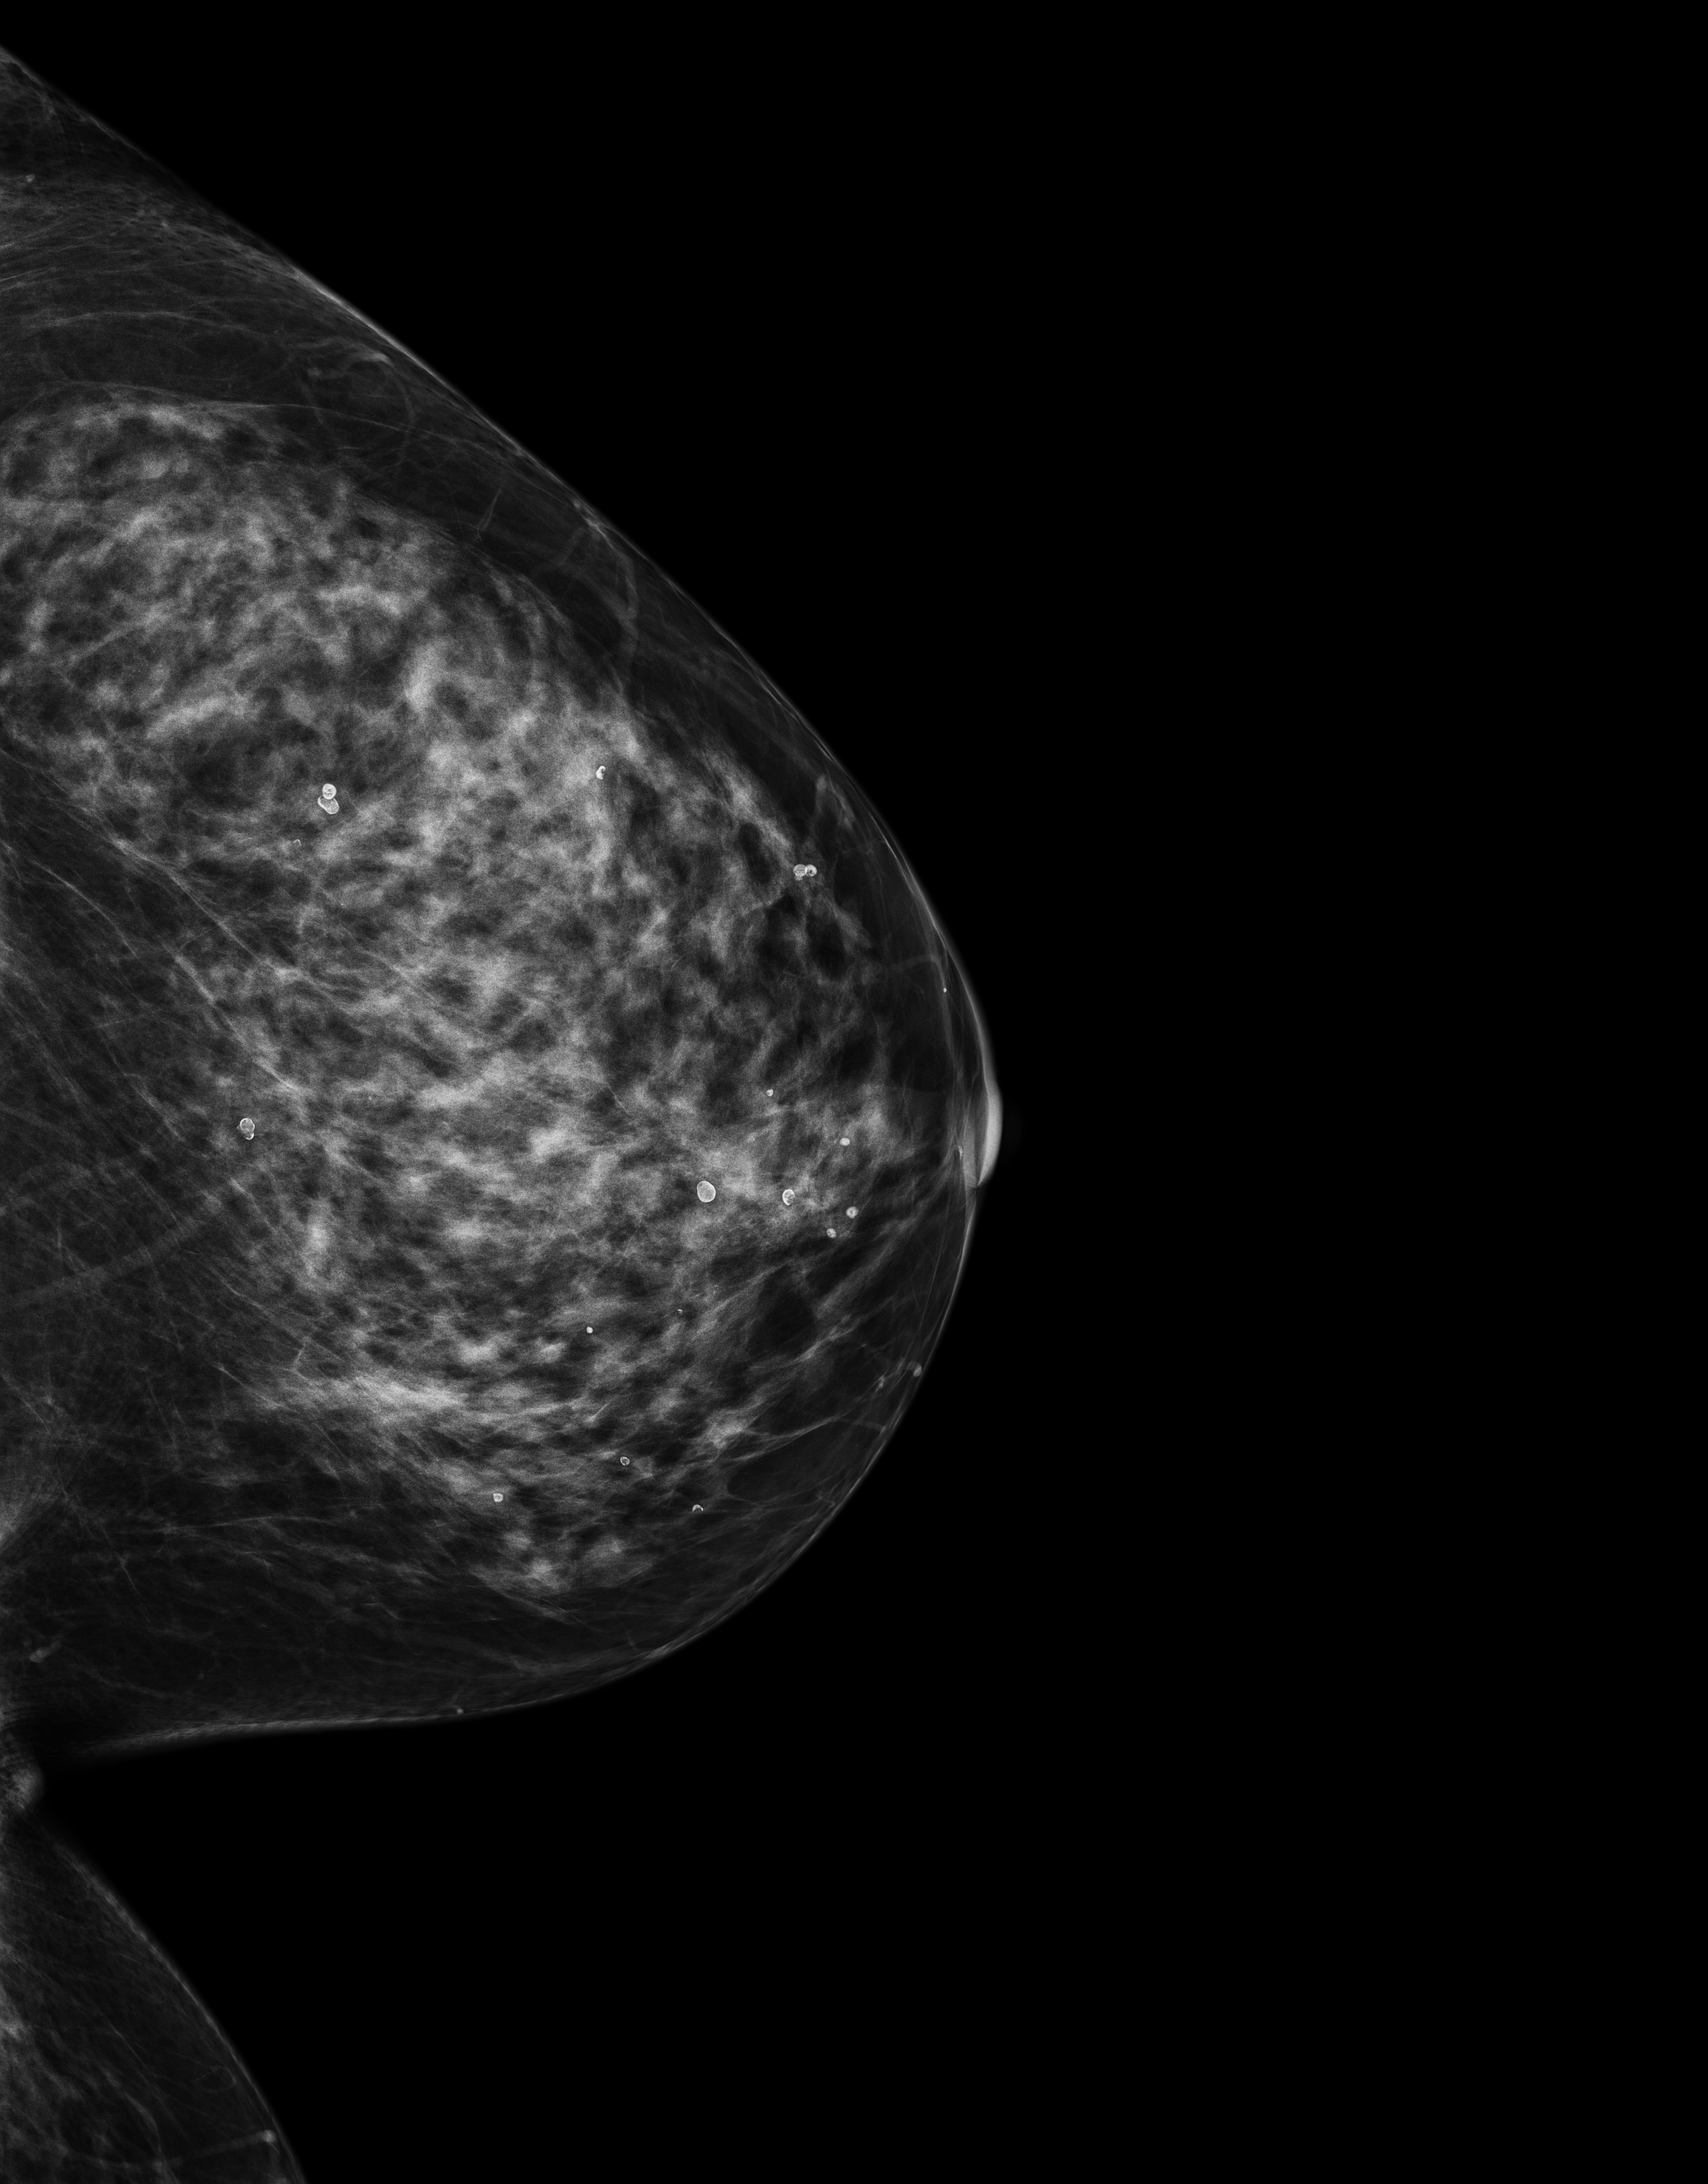
Full-field digital mammogram (FFDM); left breast; cranio-caudal projection; screening examination. Patient aged 66 years (female).
BI-RADS breast density category at the screening exam (both breasts, scale 1–4): 3. Final BI-RADS assessment for this screening round (tomosynthesis exam, both breasts): category 1. Recall: no recall after this screen.